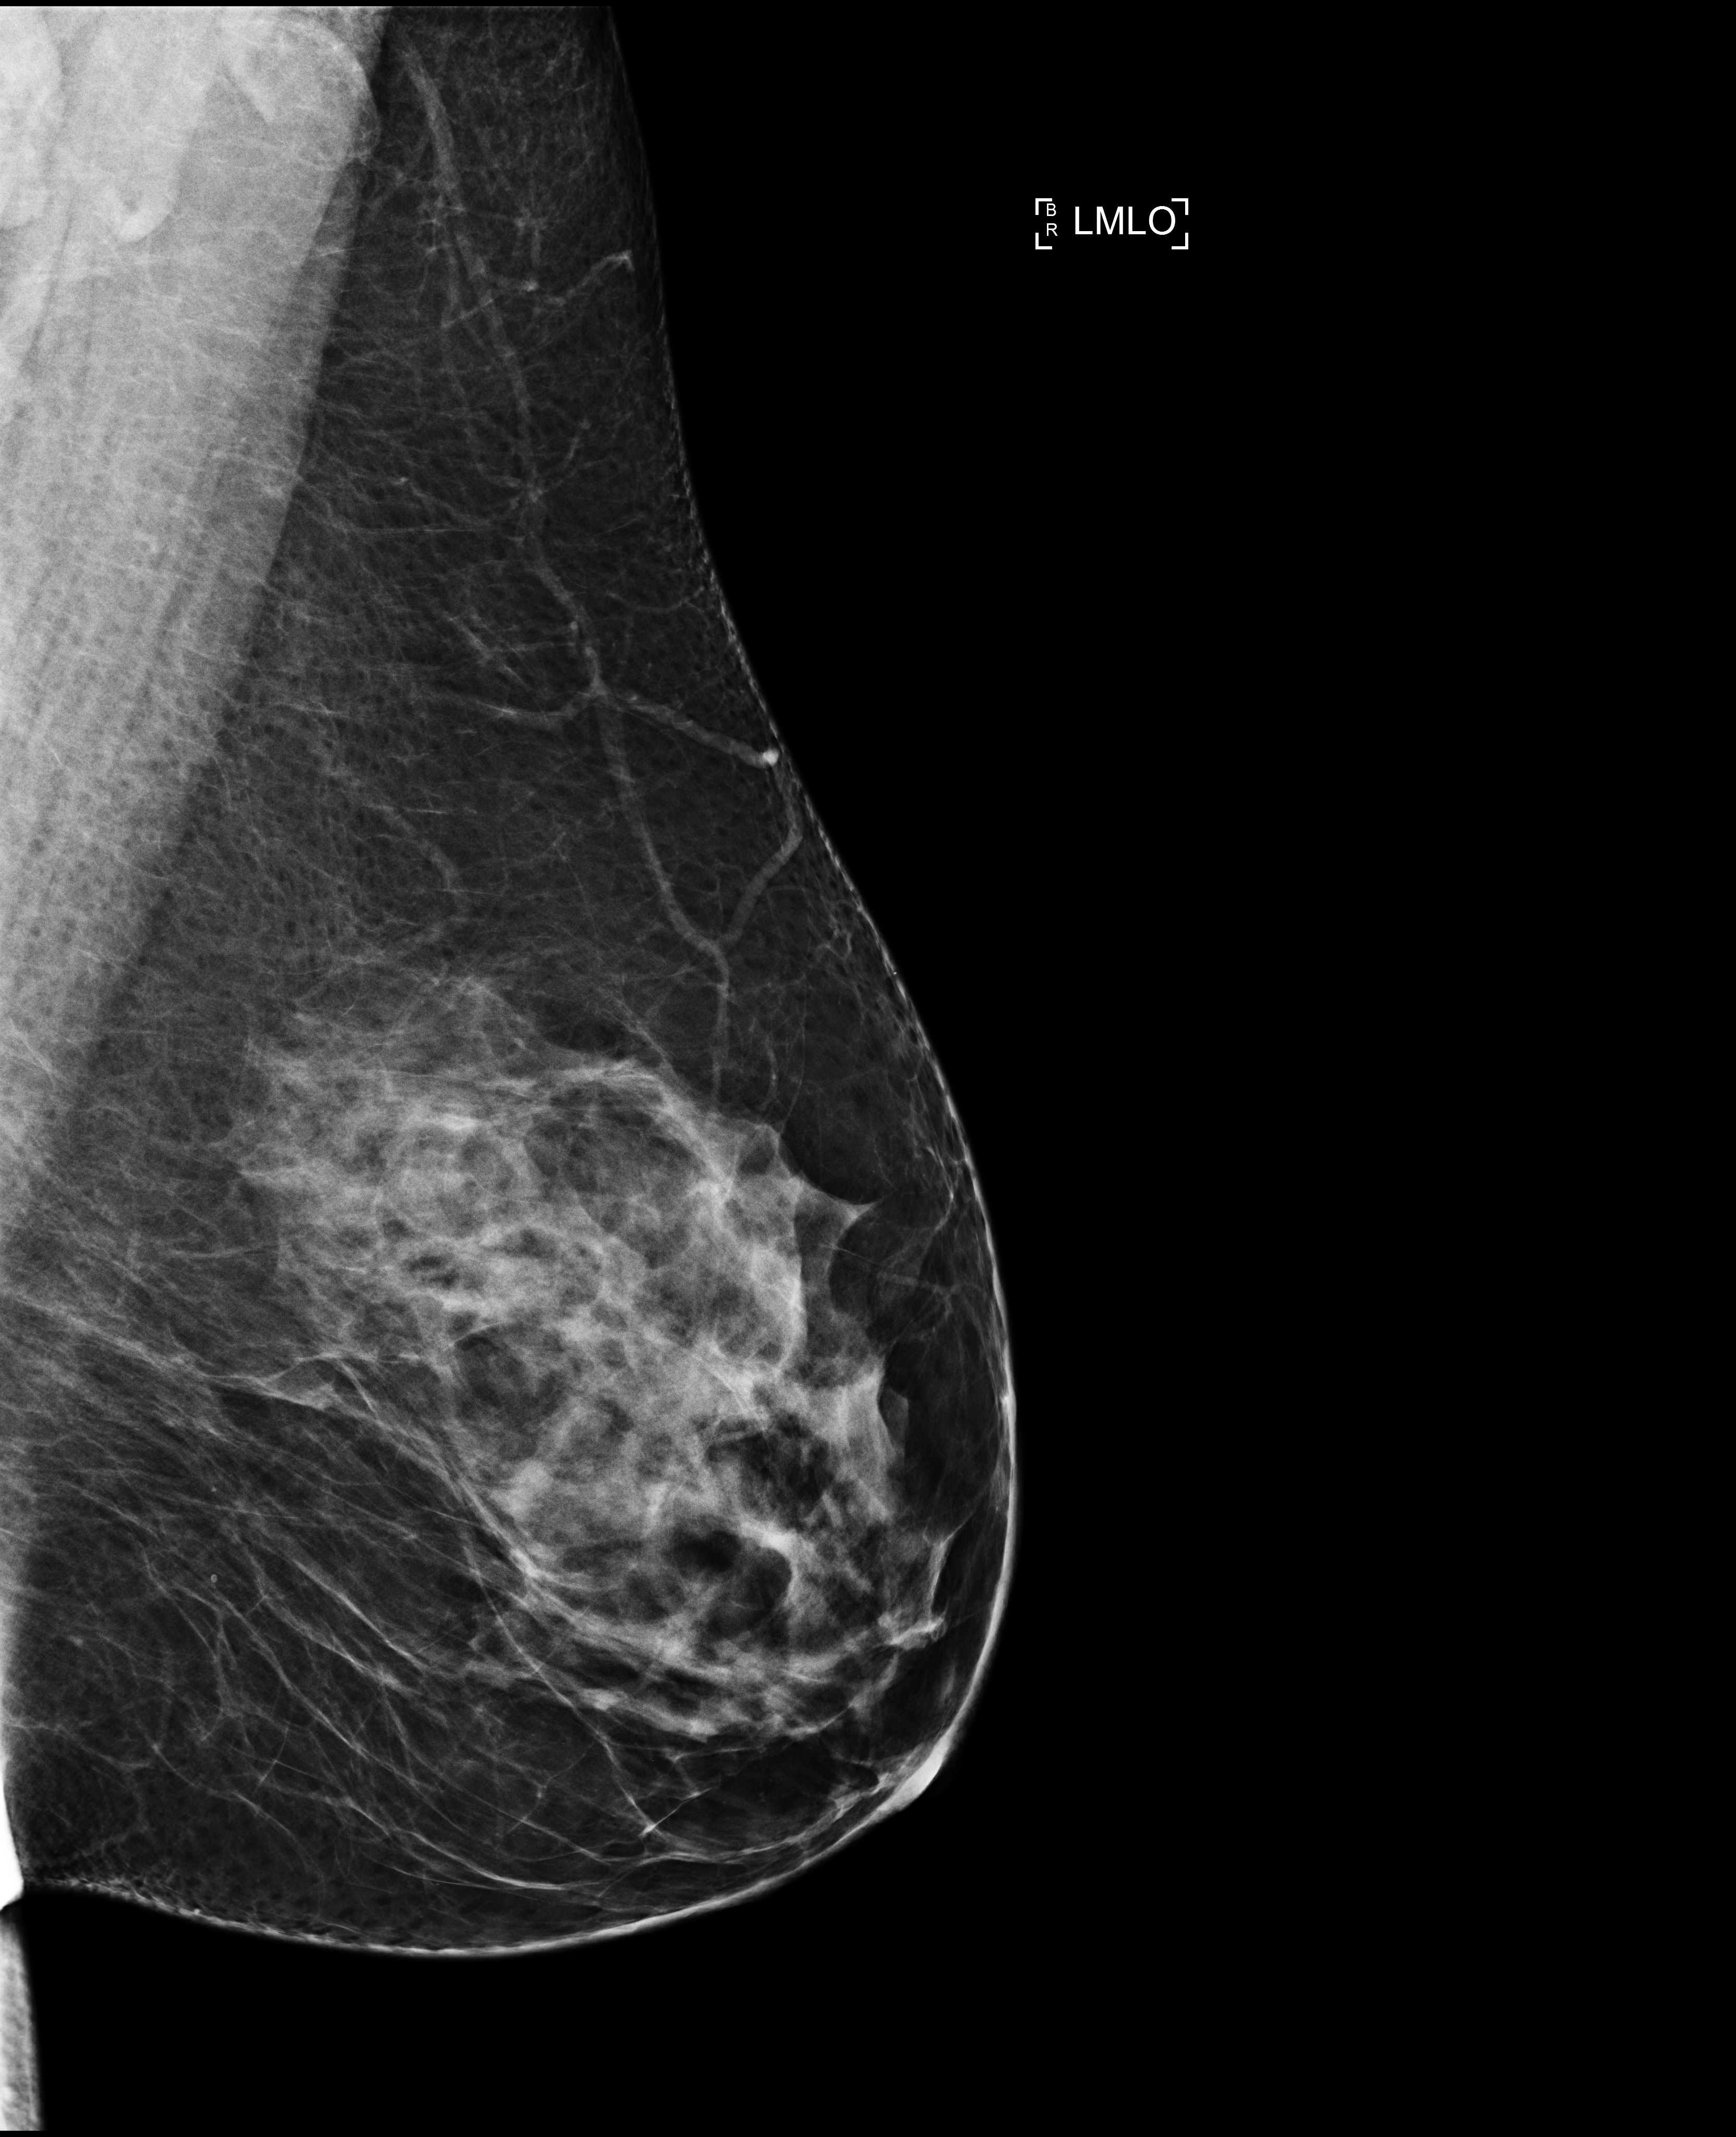
Screening examination. Patient aged 46 years (female).
Image type: full-field digital mammogram. Breast: left. Projection: mediolateral oblique (MLO) view.